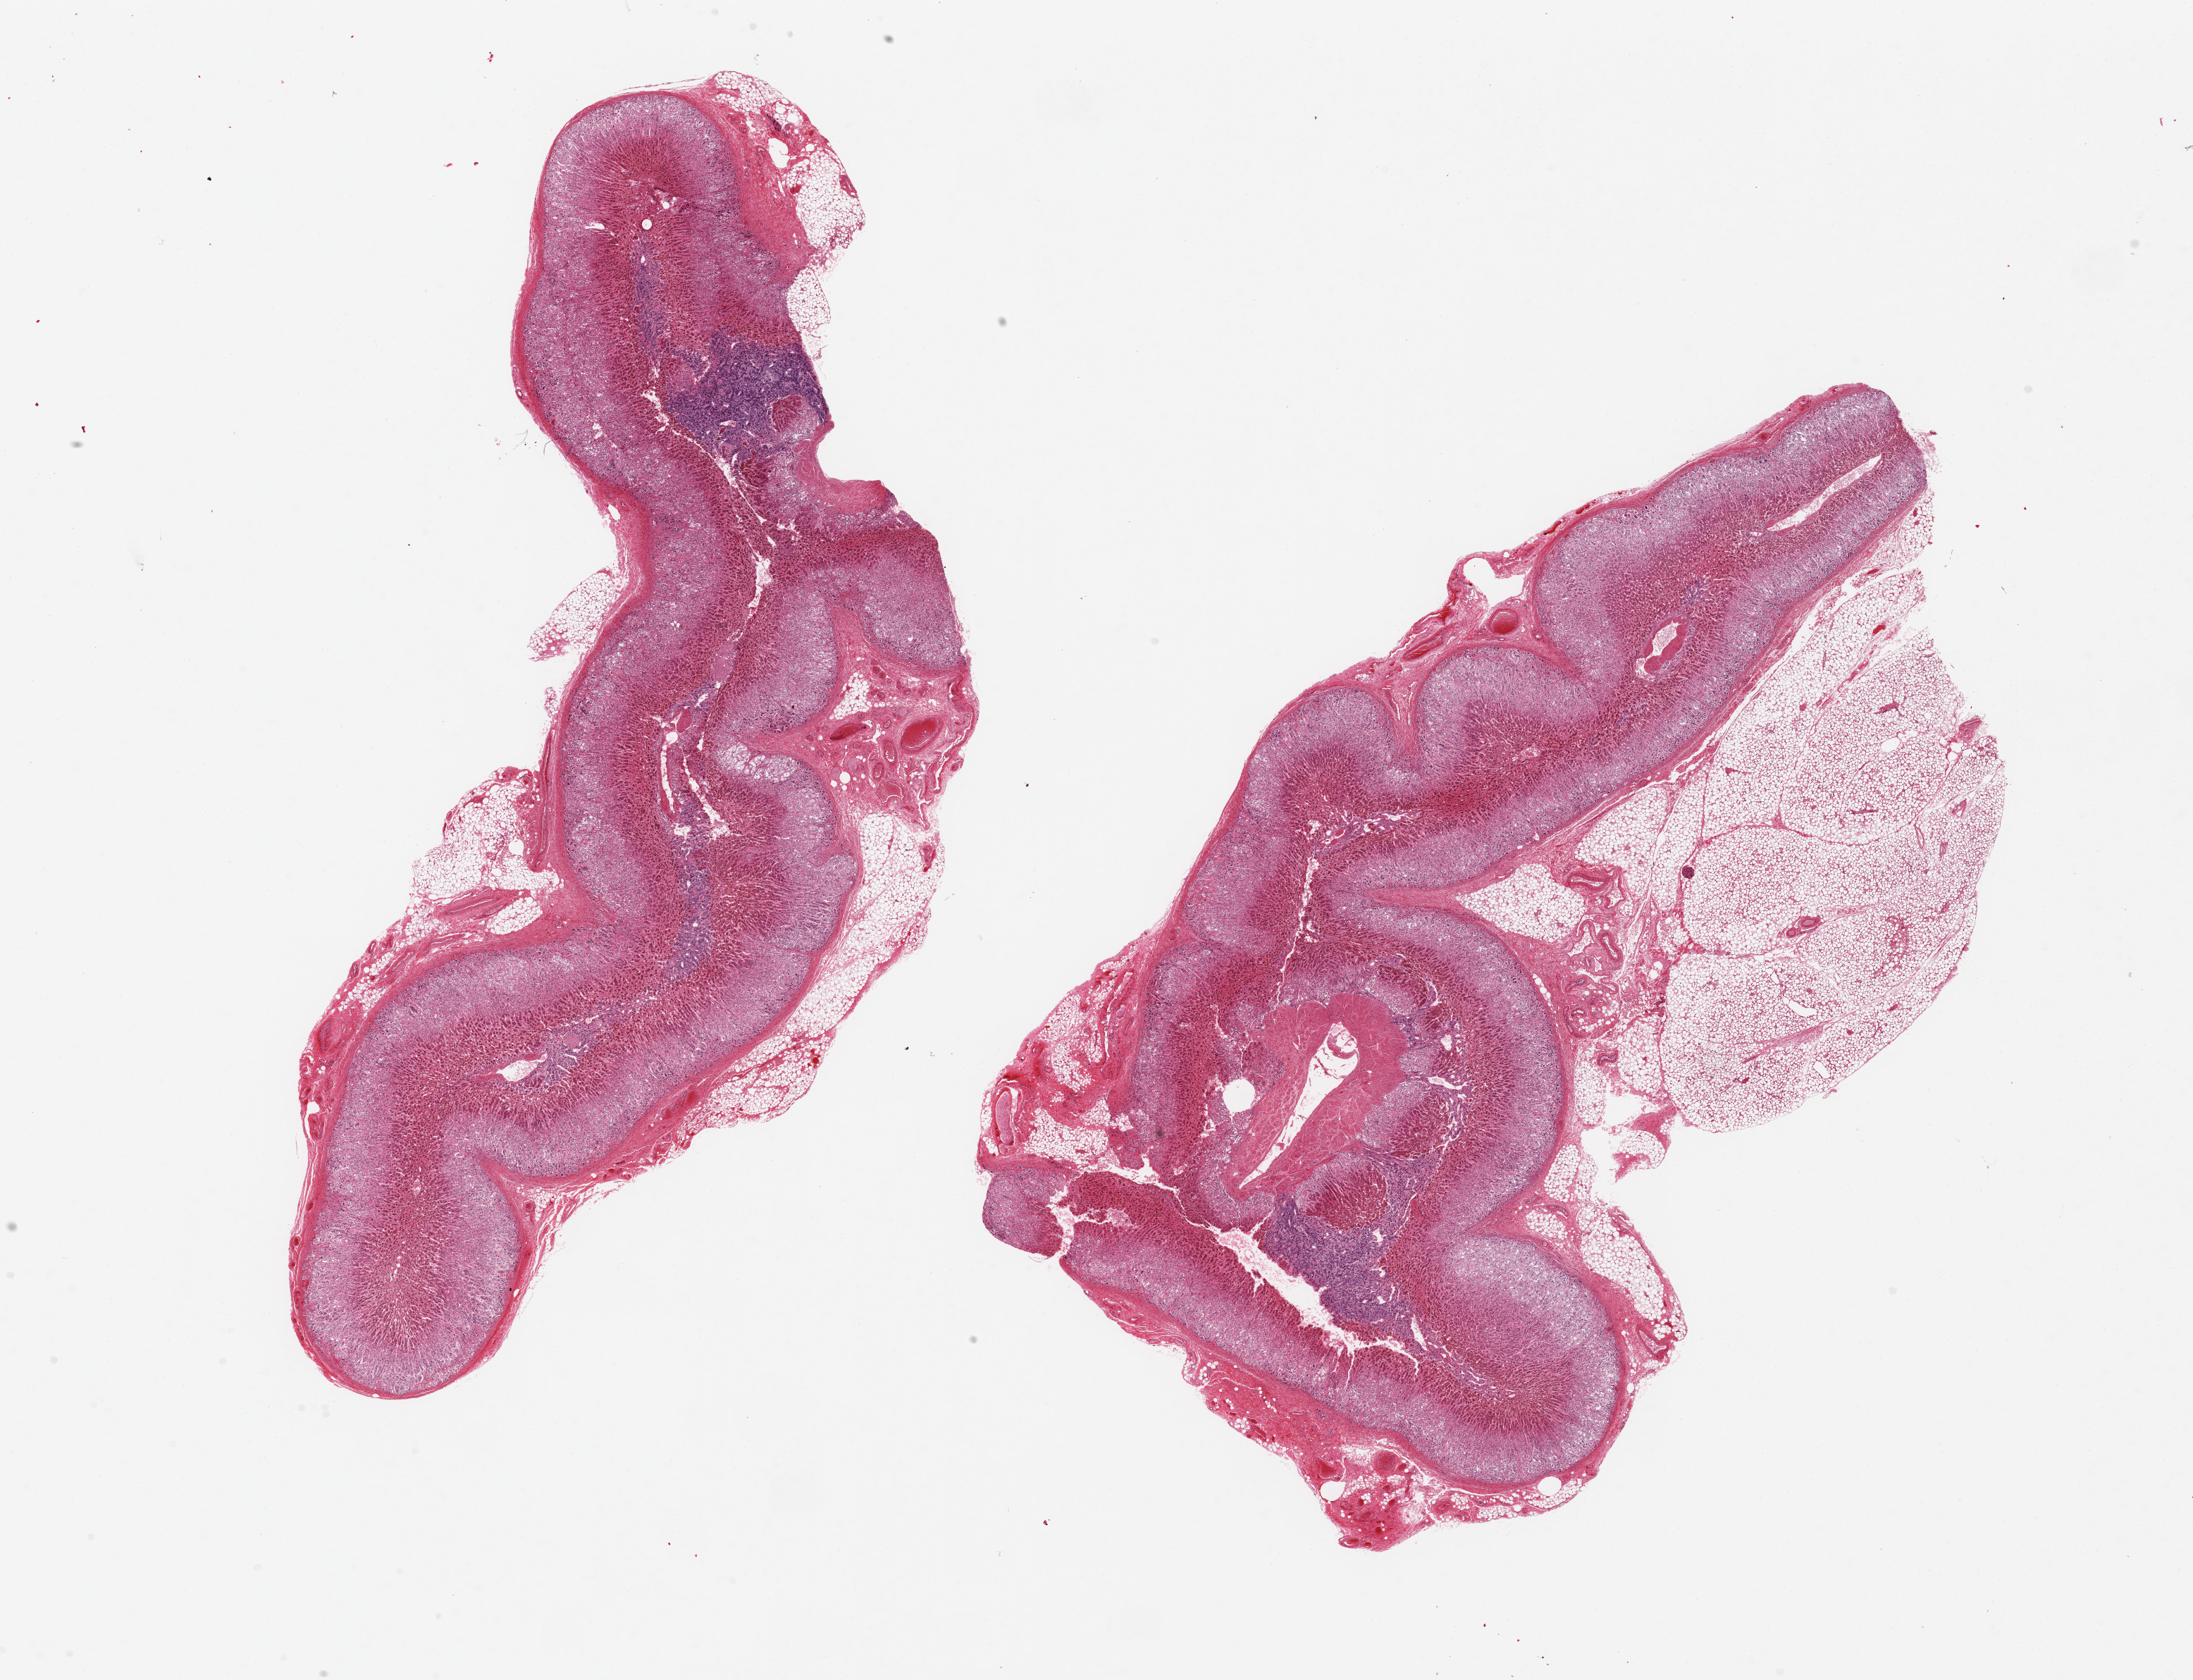
H&E whole-slide image, brightfield, a low-resolution overview of the entire scanned area, about 24.6 x 18.9 mm (from a 20x scan), PAXgene-fixed paraffin-embedded (PFPE) section, section of adrenal gland (target tissue), tissue donor sample. Male donor.
Review note (as recorded): 2 pieces 15x3 & 13x5 mm; 6x4 mm adipose on external surface of one piece; ~10% adipose on other.